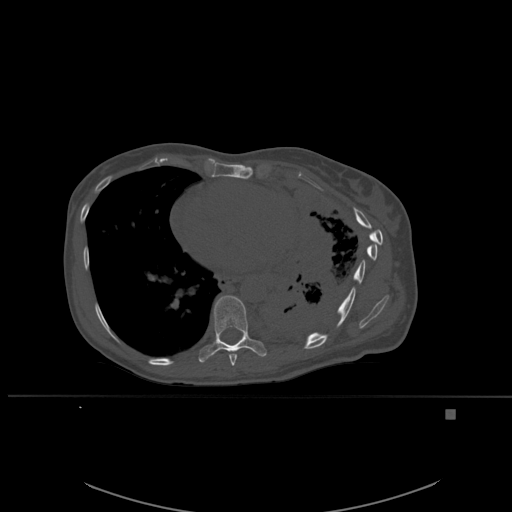
CT including the spine, one axial slice. Position 336 of 537 along the scan axis. Bone window (W 1800 / L 400 HU). 1.5 mm slice thickness. 512 × 512 image matrix, field of view 440 × 440 mm. Patient: female, 45 years. From the clinical record (not read from this slice): primary cancer: lung.
Structures marked on this image (semi-automatically segmented with operator editing):
- T8 vertebra: bounding box [x1, y1, x2, y2] px = [228, 351, 237, 366]
- T9 vertebra: [198, 295, 267, 363]